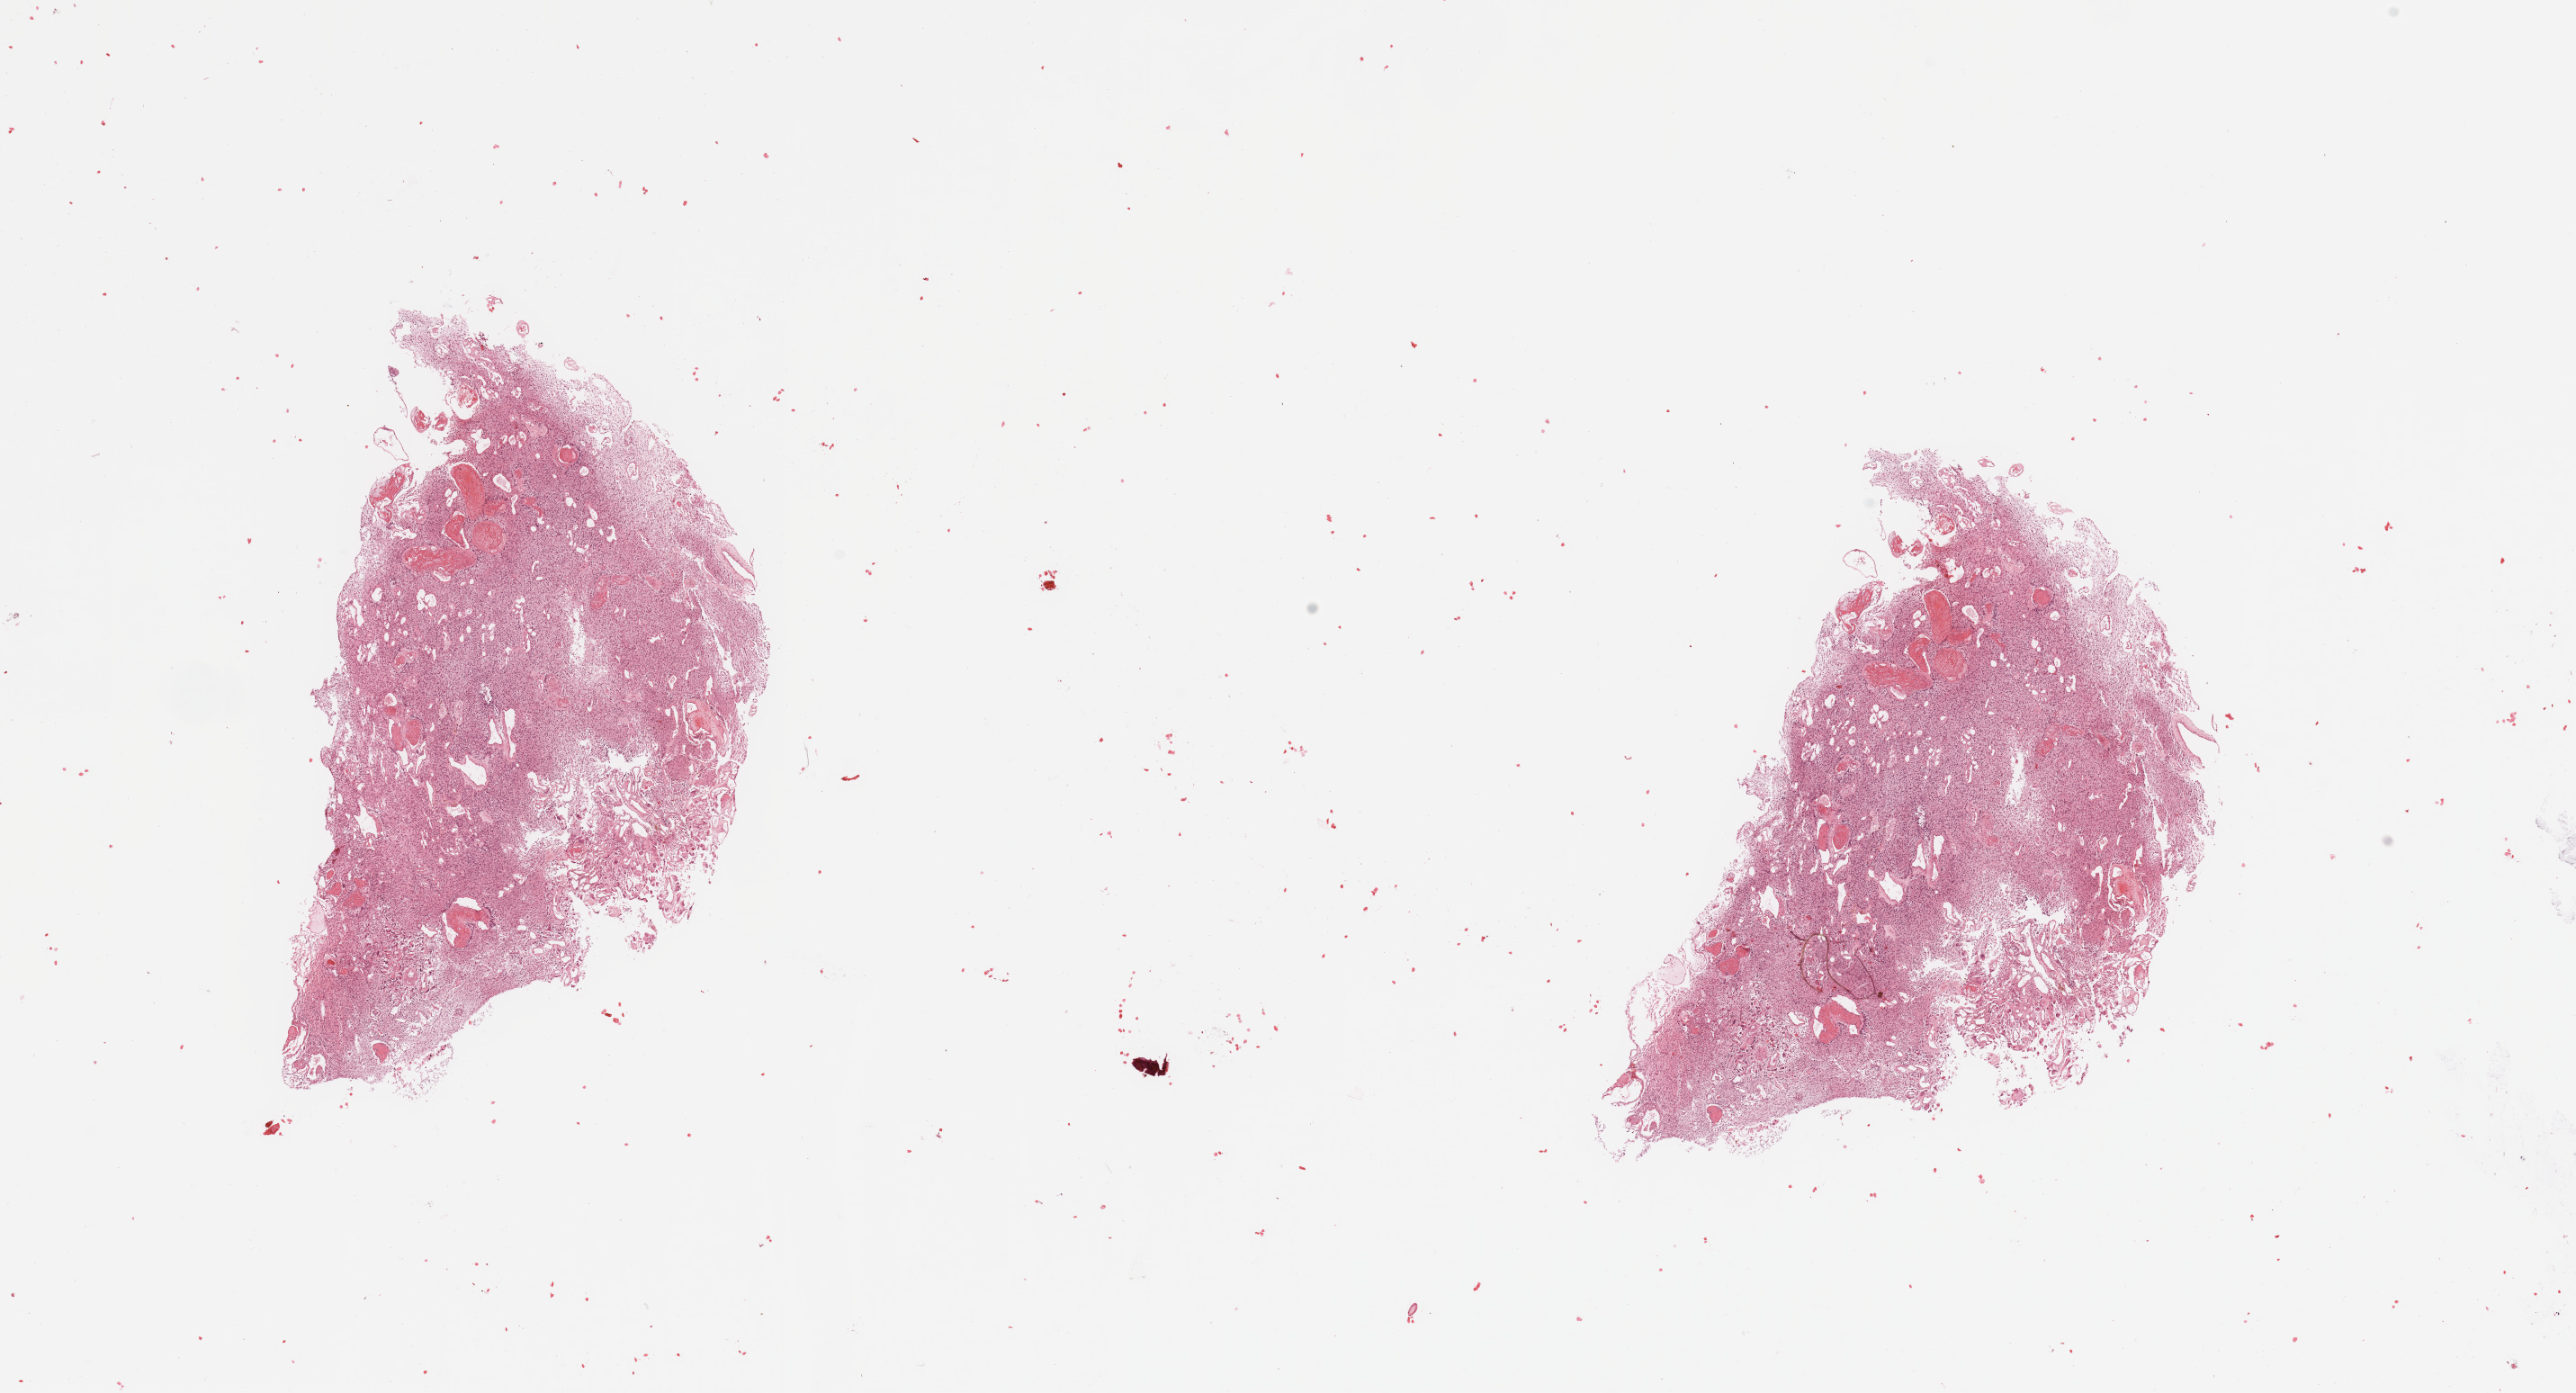
H&E whole-slide image, whole scanned area (about 22.6 x 12.2 mm, from a 20x scan) shown as a low-resolution overview. Tumour tissue sample, sampled site: frontal lobe. Male, 39 y/o. Pathologist review of this section (percent, as recorded): tumour nuclei 85%, necrosis 5%.
Histologic diagnosis: Glioblastoma. Primary tumour site (as recorded): frontal lobe.